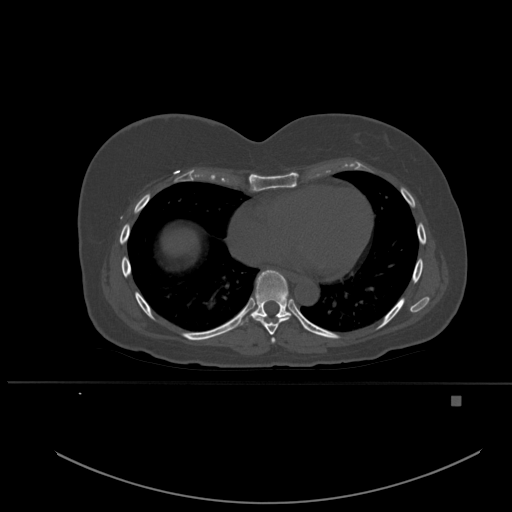
CT including the spine, one axial slice. Position 327 of 651 along the scan axis. Bone window (W 1800 / L 400 HU). 512 × 512 image matrix. Female patient, age 49 years. Case-level facts recorded for this patient, not image findings: primary cancer: breast; vertebrae with lytic lesions (as recorded): L3, T12, L4.
Annotated regions visible in this slice (semi-automatically segmented with operator editing):
- T6 vertebra: bounding box <271,338,275,343> (left, top, right, bottom; pixels)
- T7 vertebra: <253,317,289,335>
- T8 vertebra: <238,270,291,326>